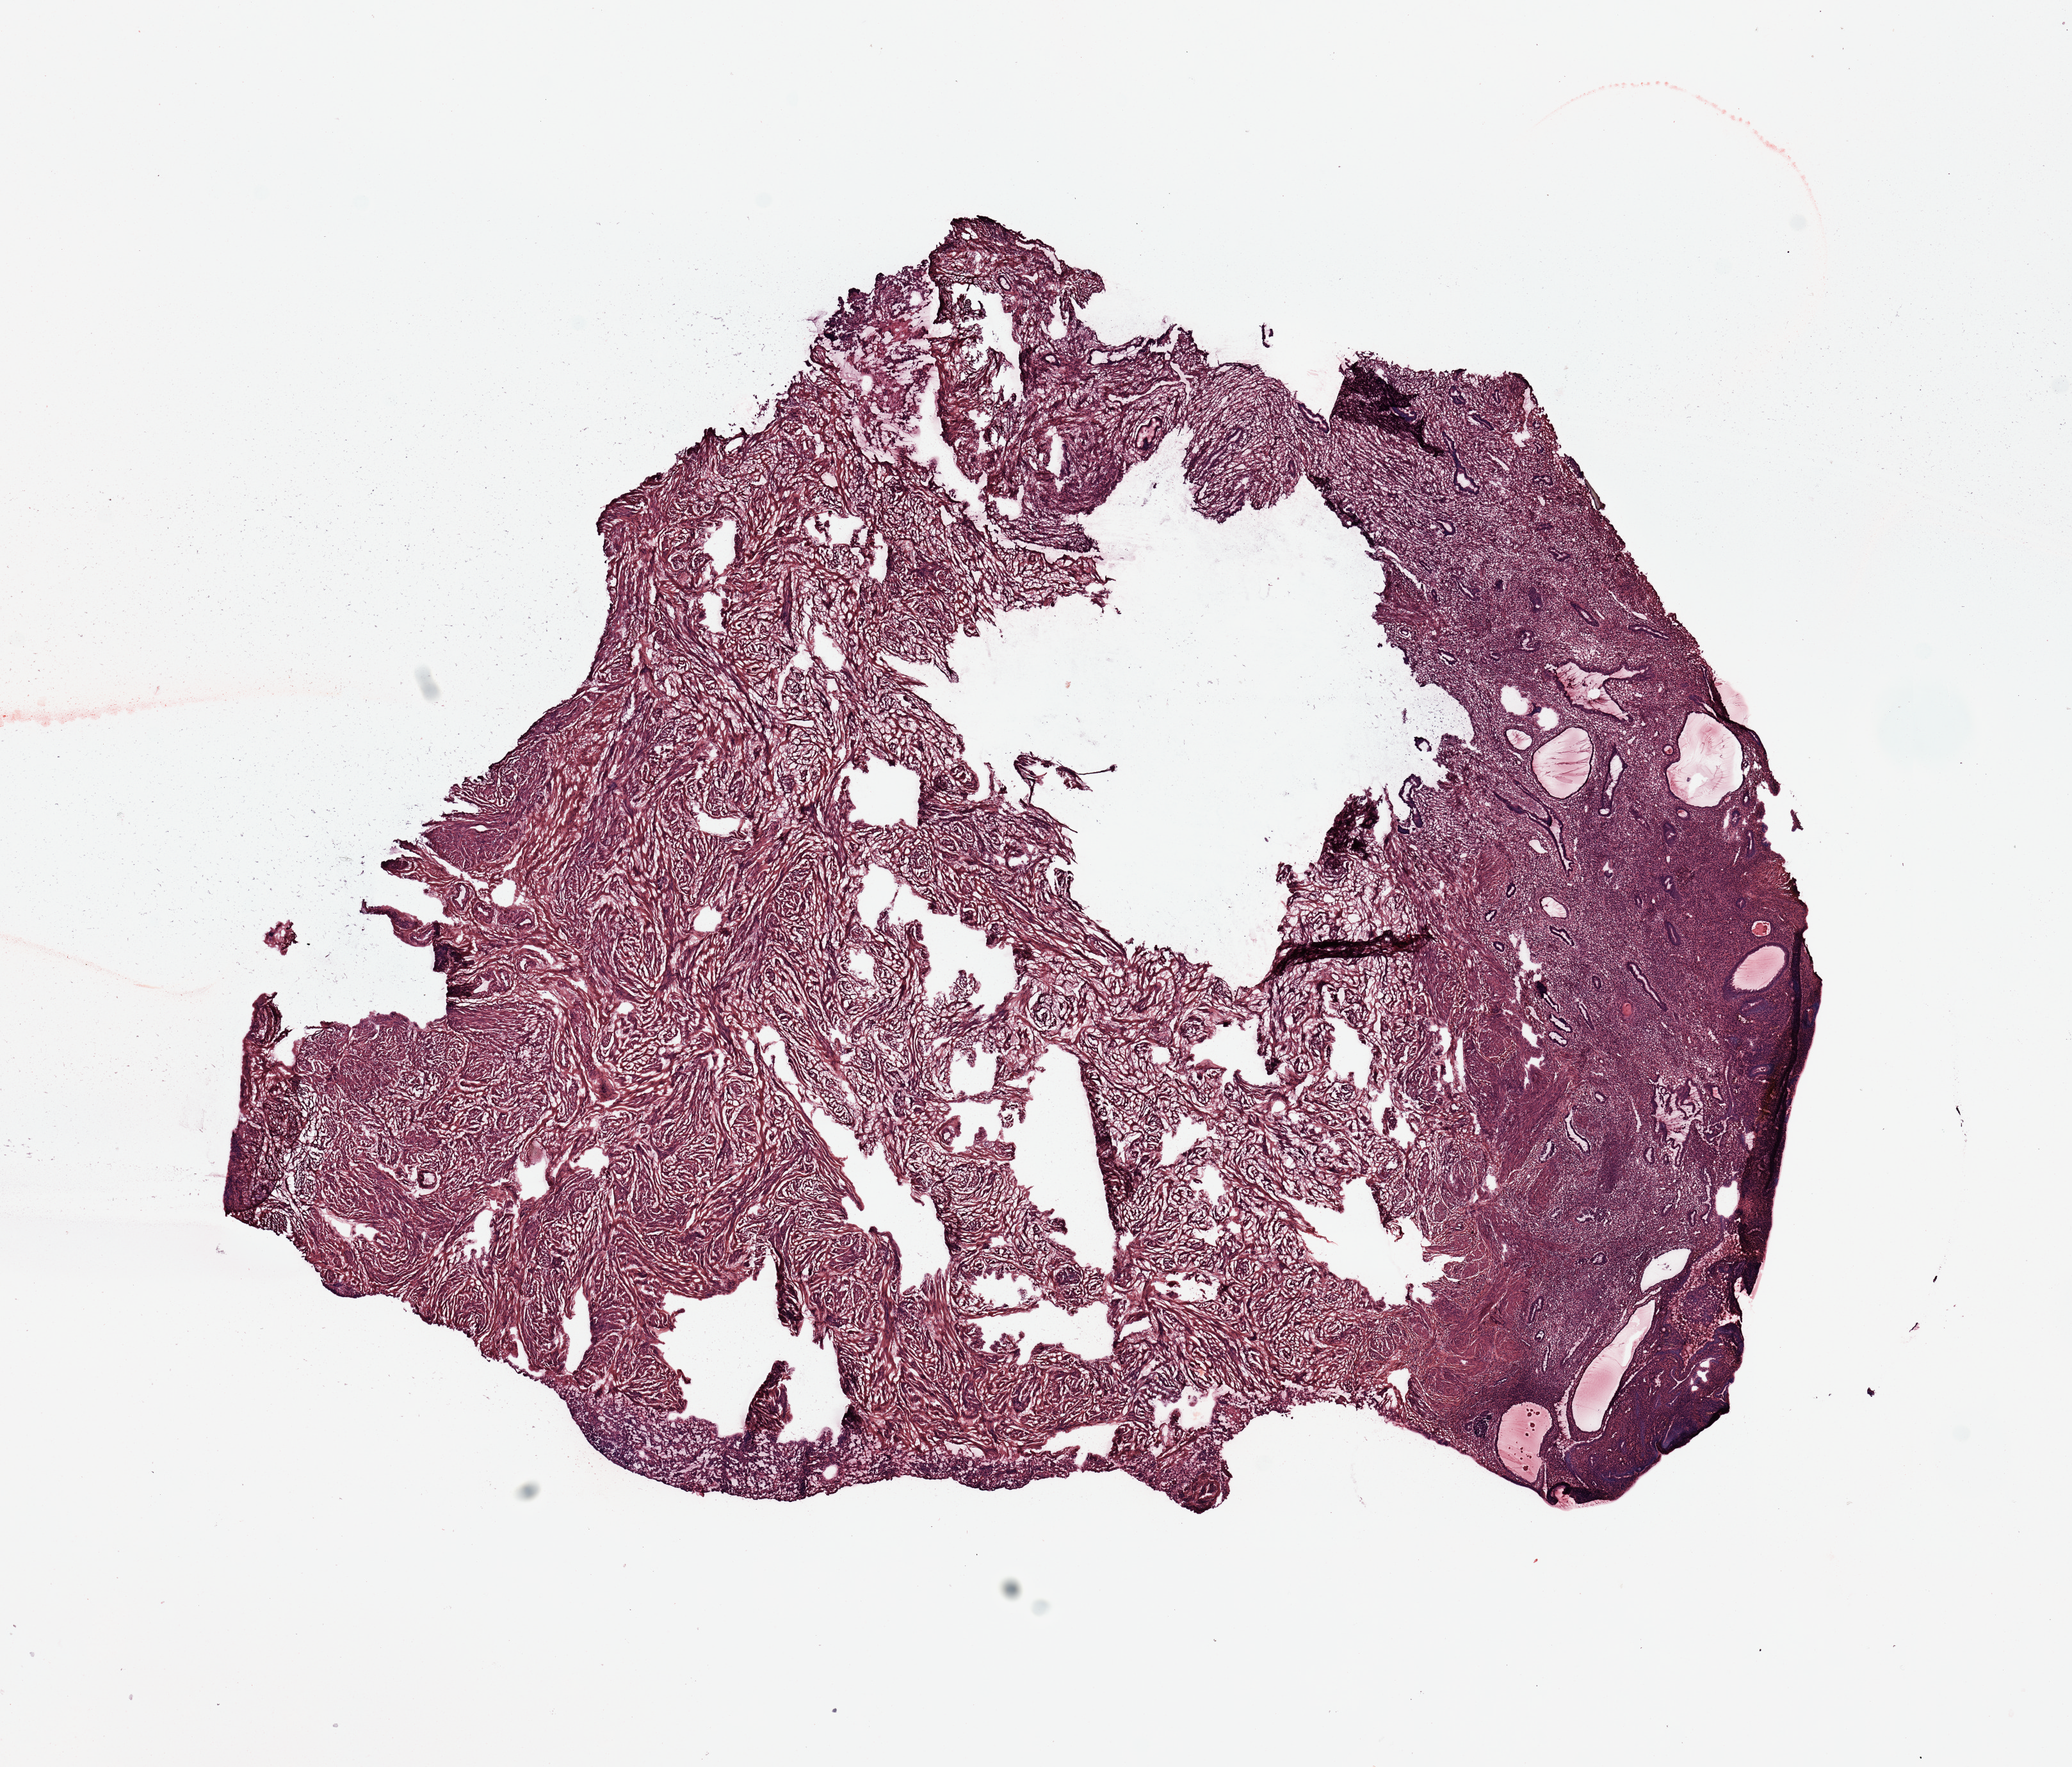
Hematoxylin and eosin (H&E) stained whole-slide image, low-resolution overview of the scanned area, about 12.8 x 10.9 mm (from a 20x scan), normal (non-tumour) tissue sample, sampled site: uterus. 65-year-old female patient.
• this section: normal (non-tumour) tissue from the same patient
• patient diagnosis: Endometrioid adenocarcinoma, NOS